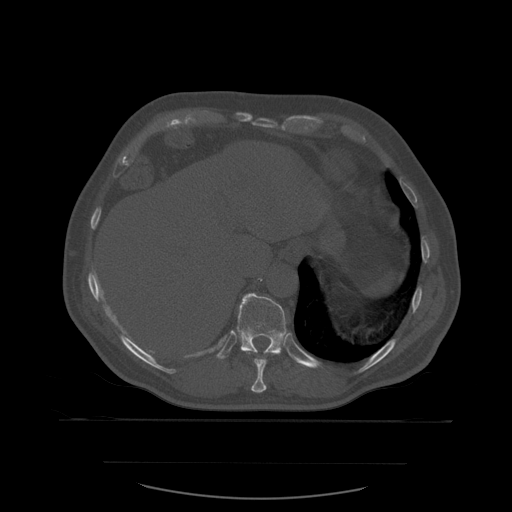
CT including the spine, one axial slice; slice 306 of 590 in the series (ordered by position); bone window (W 1800 / L 400 HU); 512 × 512 image matrix, field of view 479 × 479 mm. Patient age 71 years. From the clinical record (not read from this slice): primary cancer: lung.
Outlined on this slice (semi-automatic segmentation, software-assisted and operator-edited):
- T10 vertebra: bounding box <247,353,267,393> (left, top, right, bottom; pixels)
- T11 vertebra: <236,293,293,369>